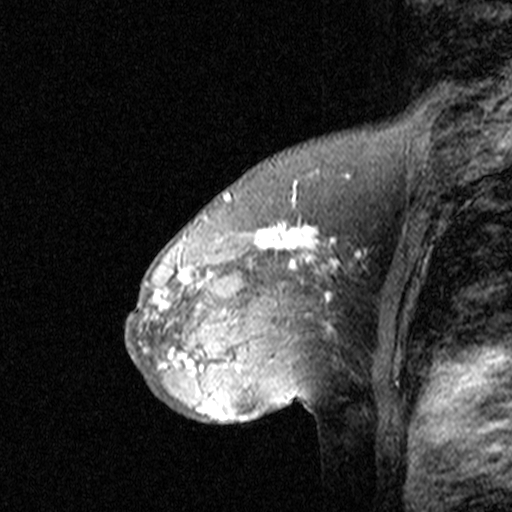
Breast MRI (dynamic contrast-enhanced), one sagittal slice. Slice 27 of 44 in the series (ordered by position). Dynamic contrast-enhanced study with each time point stored as its own series, time point 2 of 3 at this slice position (early post-contrast, ordered by acquisition time). 1.5 T. TE 4.5 ms, TR 11 ms. 512 × 512 image matrix, field of view 200 × 200 mm. Patient: female, 46 years. Case-level facts recorded for this patient, not image findings: setting: breast cancer imaged before/during neoadjuvant chemotherapy; receptor status: HER2-positive.
Annotated regions visible in this slice (semi-automatic segmentation, software-assisted and operator-edited):
- analysis volume of interest (the breast-tissue region the enhancement analysis was run in; not a lesion): bounding box <144,172,359,393> (left, top, right, bottom; pixels)
- tumour enhancement mask (voxels above the 90 % enhancement threshold inside the analysis volume of interest): <145,175,347,358>